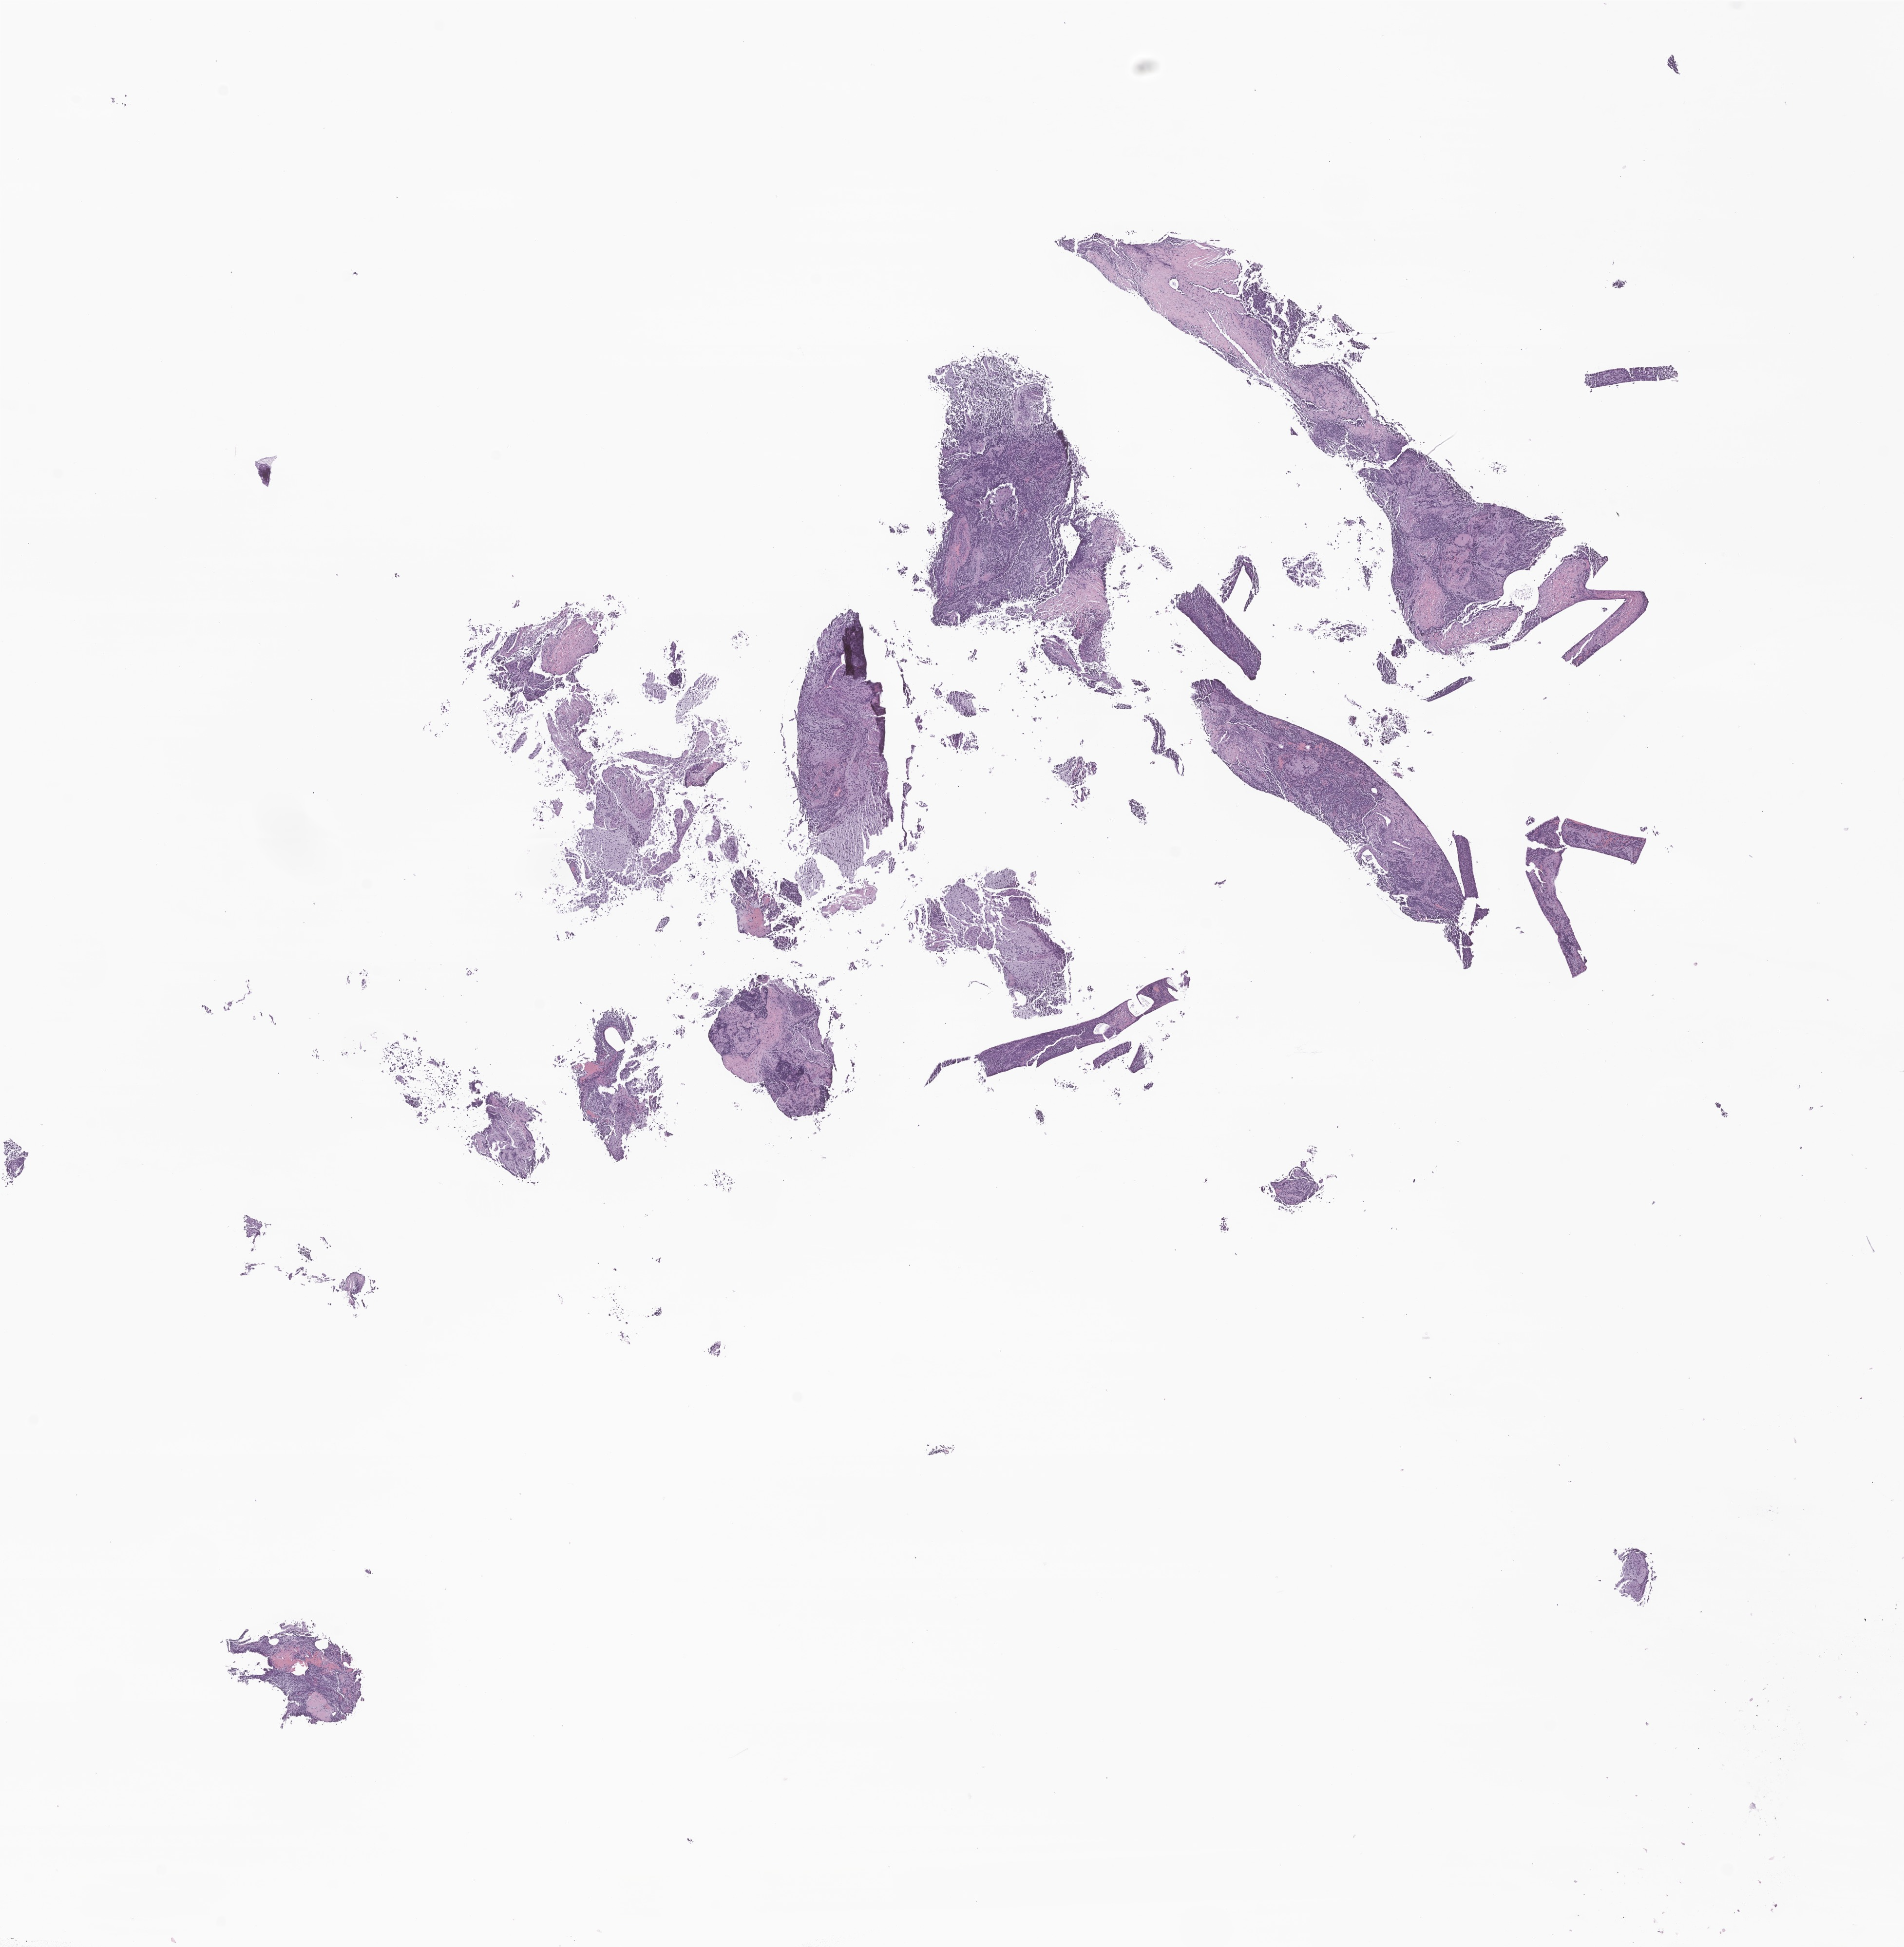
Whole-slide image, haematoxylin and eosin stain of tumor tissue from the spinal cord — low-resolution overview of the scanned area, about 16.5 x 16.8 mm. FFPE section. Male patient, age 47 months (3 years 11 months).
• recorded diagnosis: Neuroblastoma, NOS